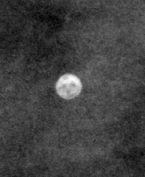
Crop from a digitized film mammogram around one marked abnormality; right breast; CC view.
Finding: calcifications, morphology round and regular / lucent center / punctate, distribution diffusely scattered; BI-RADS assessment category 2; subtlety rating 5 on a 1 (subtle) to 5 (obvious) scale; benign without callback (not worked up further).